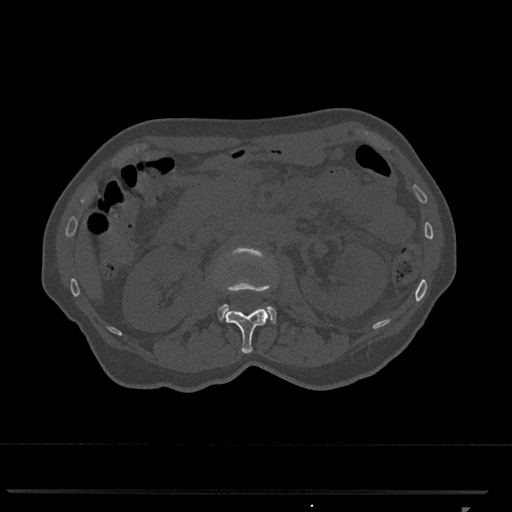
CT including the spine, one axial slice; position 377 of 793 along the scan axis; 120 kVp; bone window (W 1800 / L 400 HU); 512 × 512 image matrix, field of view 380 × 380 mm. Patient: female, 62 years. Case-level facts recorded for this patient, not image findings: primary cancer: renal.
Annotated regions visible in this slice (semi-automatic segmentation, software-assisted and operator-edited):
- L1 vertebra: bounding box (x1, y1, x2, y2) in pixels: (225, 247, 268, 354)
- L2 vertebra: (218, 247, 277, 324)